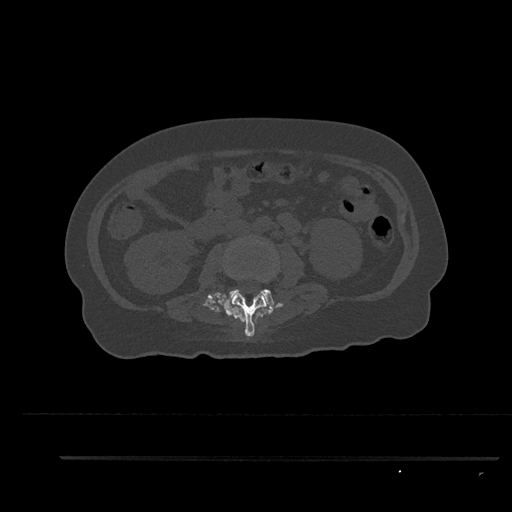
CT including the spine, one axial slice. Position 125 of 797 along the scan axis. Reconstruction kernel Br40s/3. Bone window (W 1800 / L 400 HU). 0.5 mm slice thickness. 512 × 512 image matrix, field of view 408 × 408 mm. Patient: female, 44 years. From the clinical record (not read from this slice): primary cancer: renal.
Structures marked on this image (semi-automatically segmented with operator editing):
- L2 vertebra: bounding box [x1, y1, x2, y2] px = [226, 292, 268, 337]
- L3 vertebra: [223, 239, 276, 307]